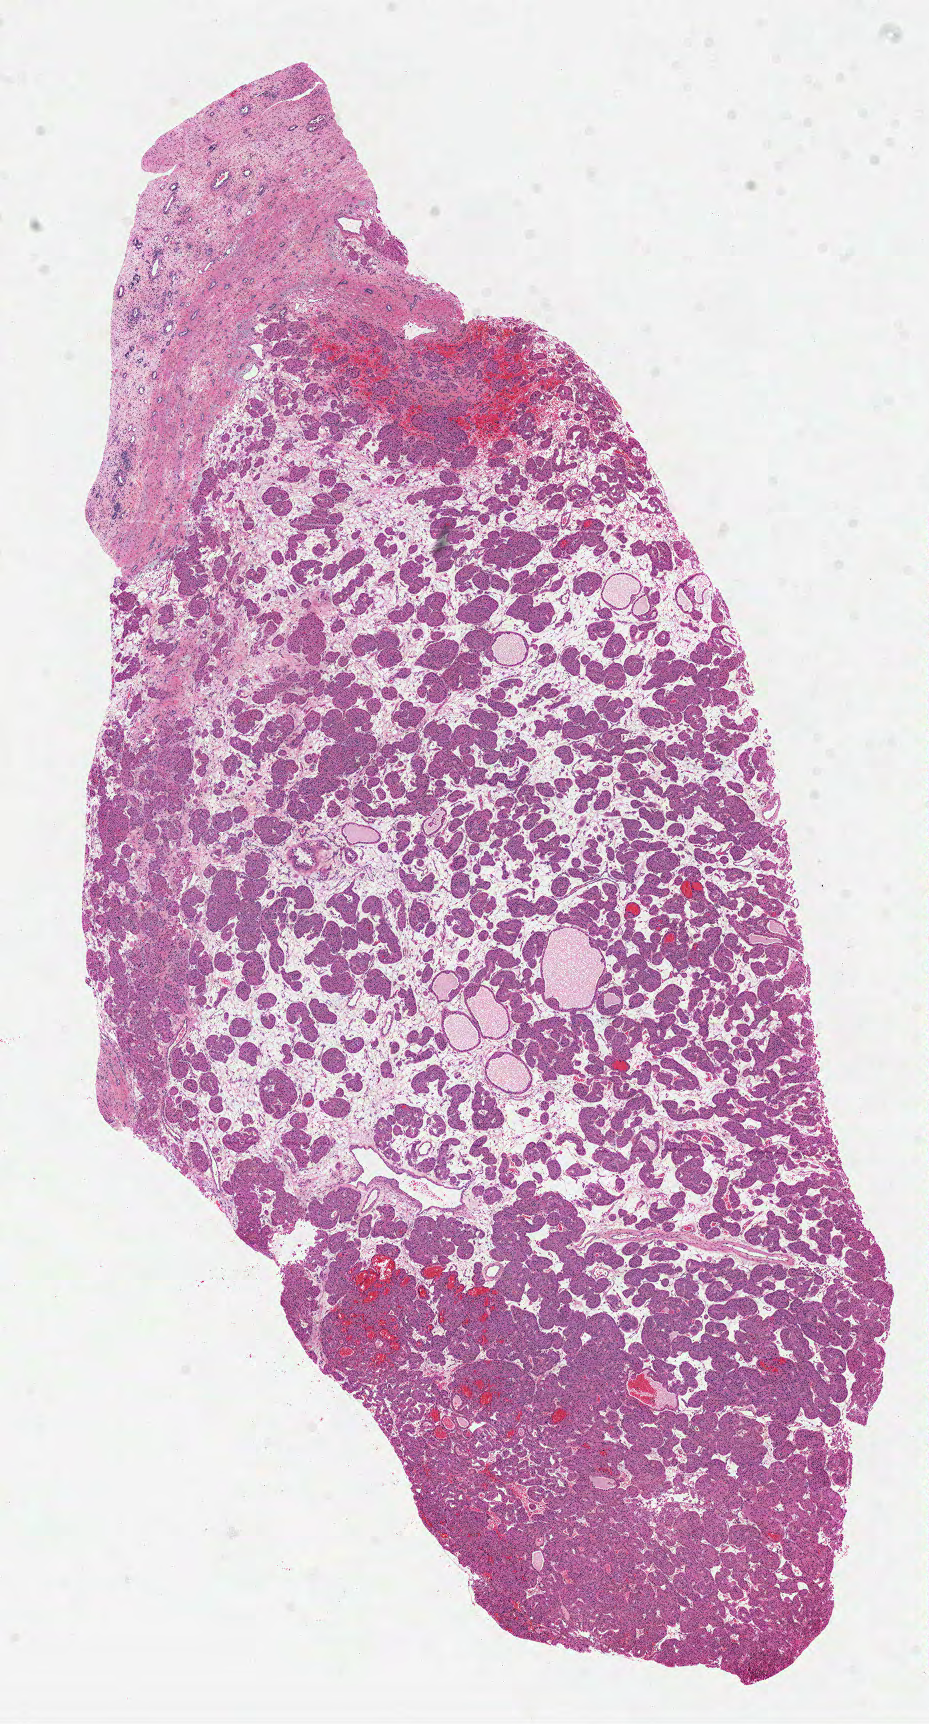
Hematoxylin and eosin (H&E) stained whole-slide image — low-resolution overview of the scanned area, about 7.5 x 13.9 mm, formalin-fixed paraffin-embedded (FFPE) diagnostic section, kidney, primary tumour sample. Patient: male, age at initial diagnosis 58 years.
Histologic diagnosis: Clear cell adenocarcinoma, NOS.